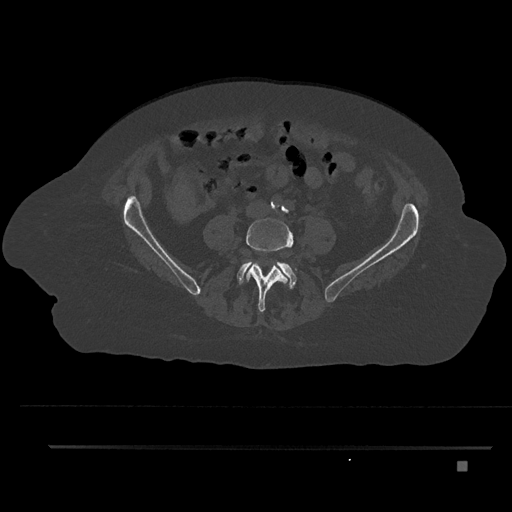
CT including the spine, one axial slice; position 68 of 797 along the scan axis; 120 kVp; bone window (W 1800 / L 400 HU); 0.5 mm slice thickness; 512 × 512 image matrix, field of view 437 × 437 mm. Female patient, age 76 years. From the clinical record (not read from this slice): primary cancer: lung; vertebrae with lytic lesions (as recorded): T11, L3.
Structures marked on this image (semi-automatically segmented with operator editing):
- L4 vertebra: box from (x=246, y=218) to (x=297, y=312) px
- L5 vertebra: (x=237, y=261)–(x=297, y=288)